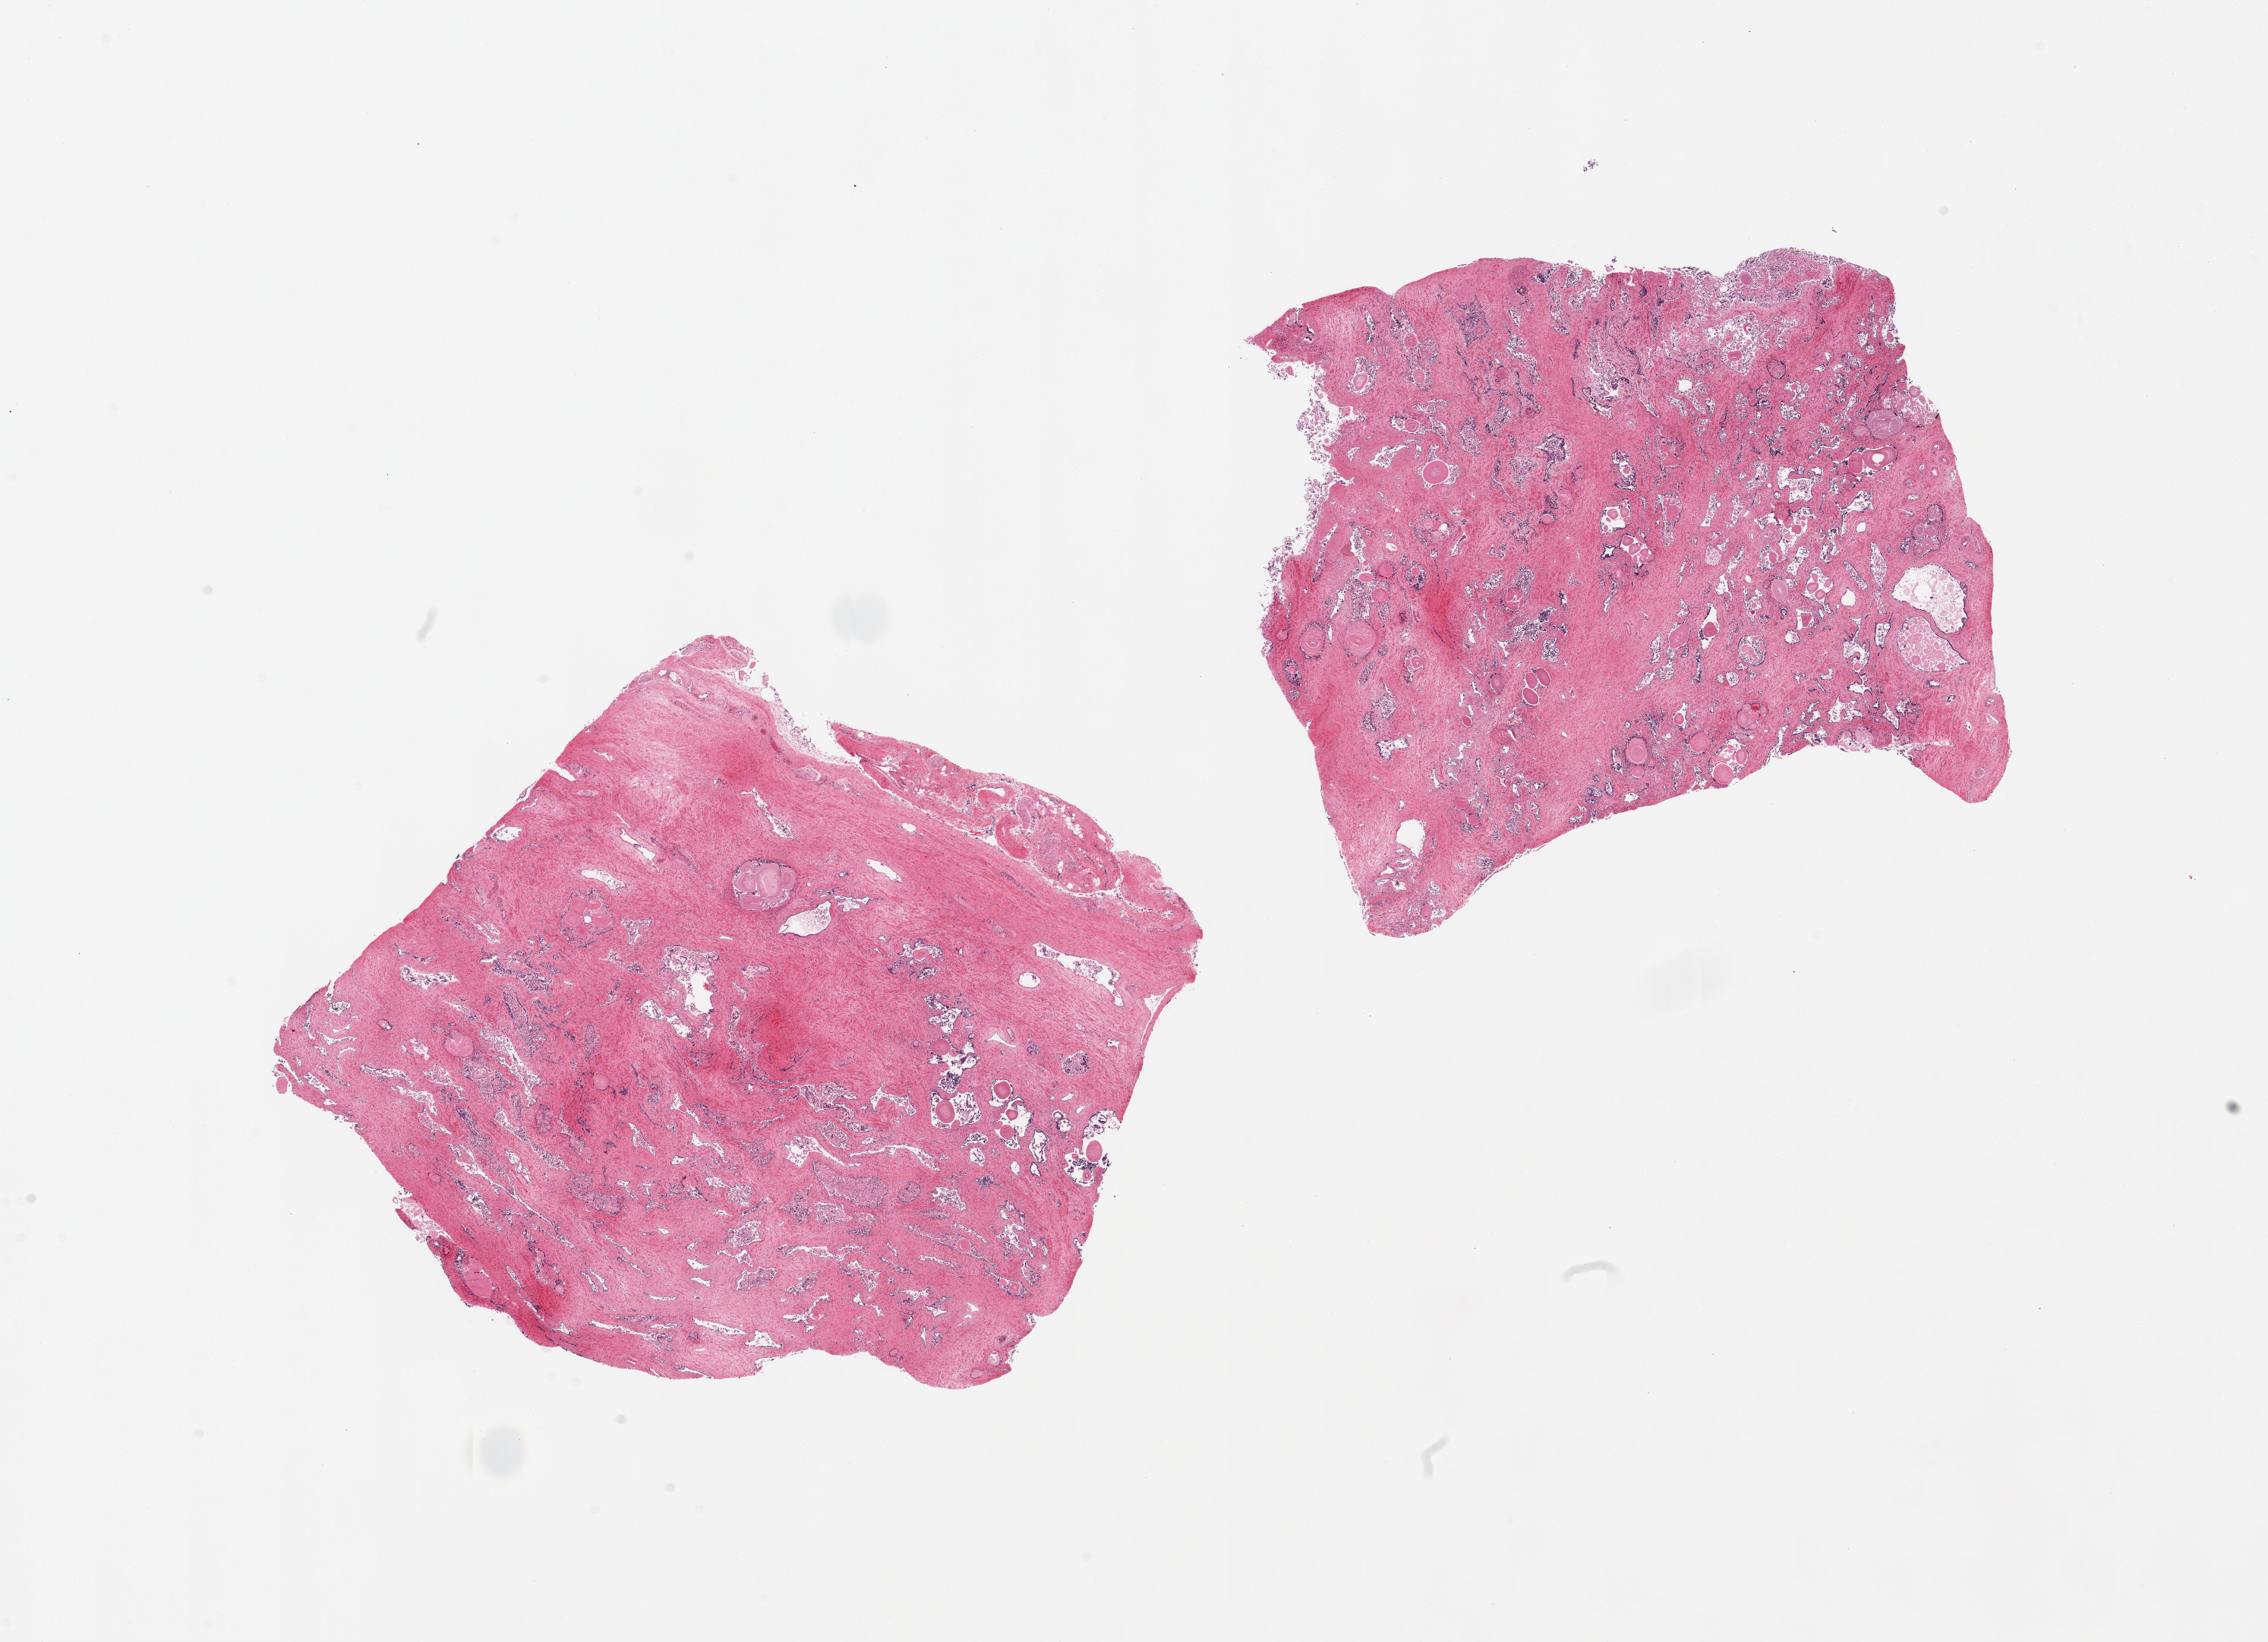
Haematoxylin and eosin whole-slide image — low-resolution overview of the scanned area, about 23.6 x 17.1 mm (acquisition: 20x scan). PAXgene-fixed paraffin-embedded (PFPE) section. Target tissue: prostate. Tissue donor sample. Male donor.
Review note (as recorded): 2 pieces, glandular elements with advanced autolysis.